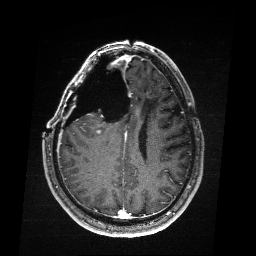
Brain MRI from a brain-tumour surgery series, one axial slice. Slice 73 of 176 in the series (ordered by position). T1-weighted post-contrast. 1 mm slice thickness. 256 × 256 image matrix, field of view 256 × 256 mm. From the clinical record (not read from this slice): histopathology: Astrocytoma; WHO grade: 4; IDH mutation: yes.
Annotated regions visible in this slice (manually delineated by an expert):
- residual tumour: box from (x=99, y=128) to (x=105, y=133) px